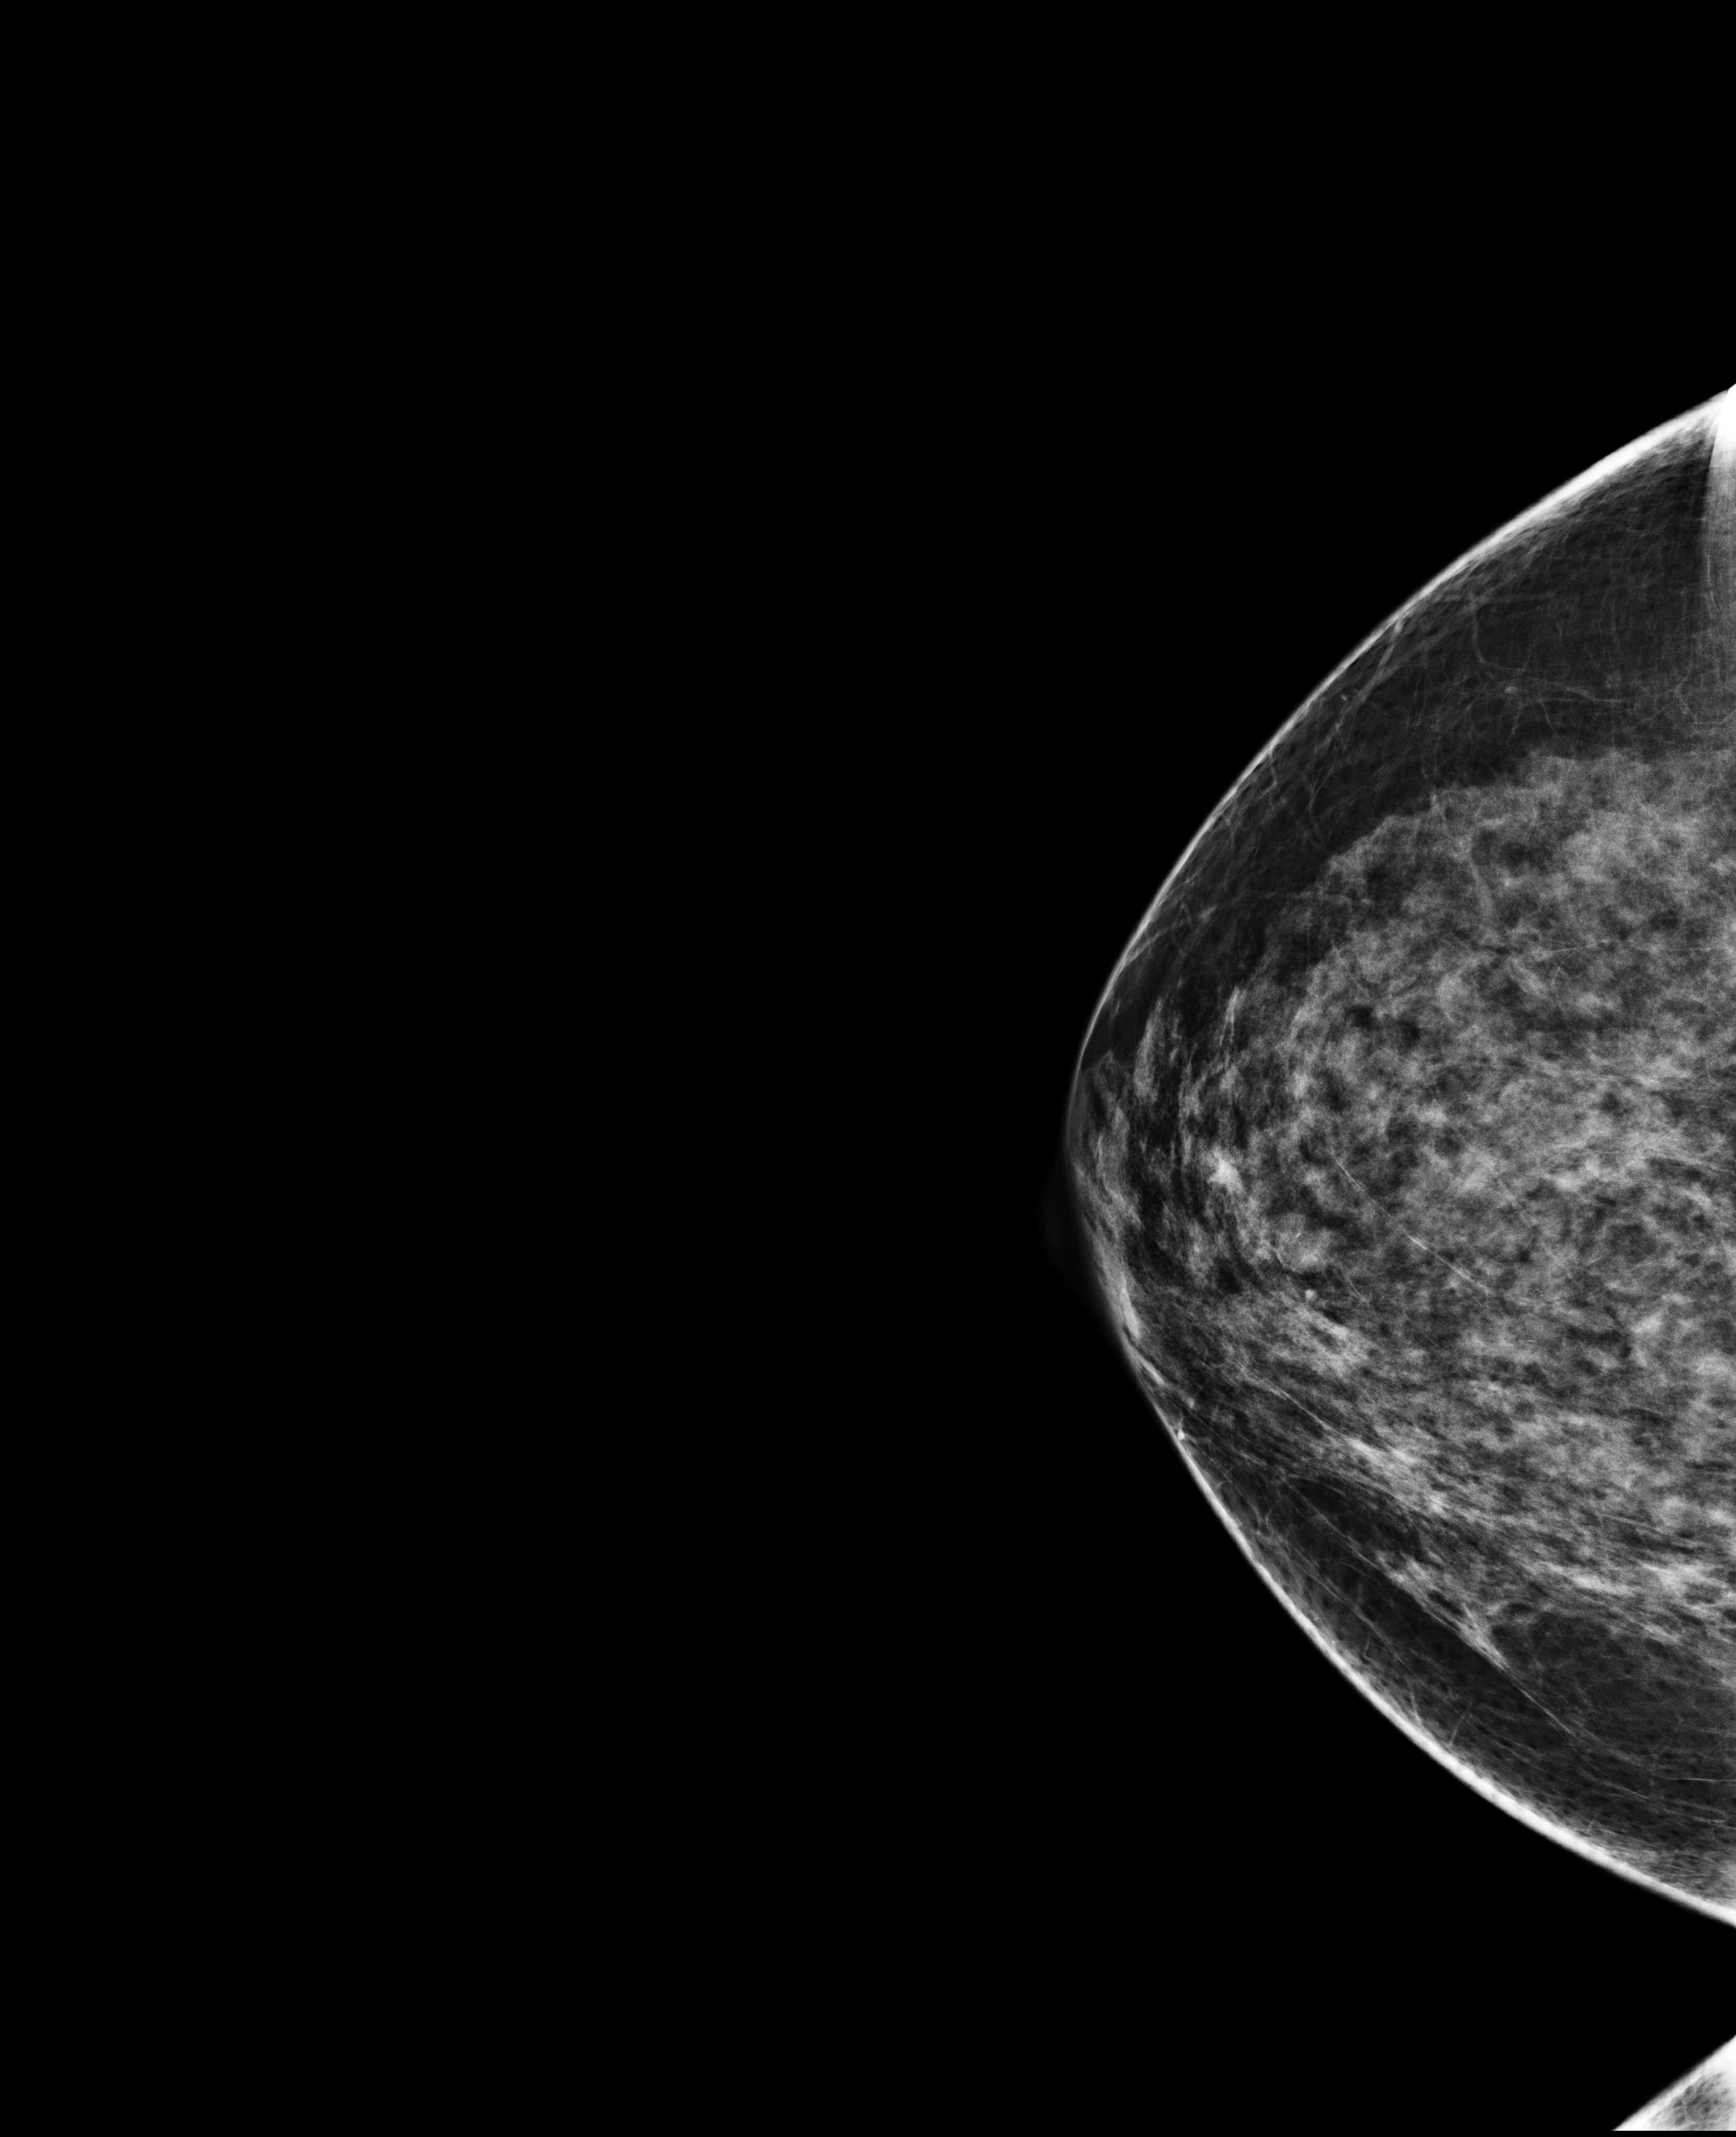
Full-field digital mammogram (FFDM); right breast; craniocaudal (CC) view; screening examination; compressed breast thickness 66 mm. Patient aged 52 years (female).
BI-RADS breast density category at the screening exam (both breasts, scale 1–4): 3. Final BI-RADS assessment for this screening round (tomosynthesis exam, both breasts): category 1. Recall: no recall after this screen.